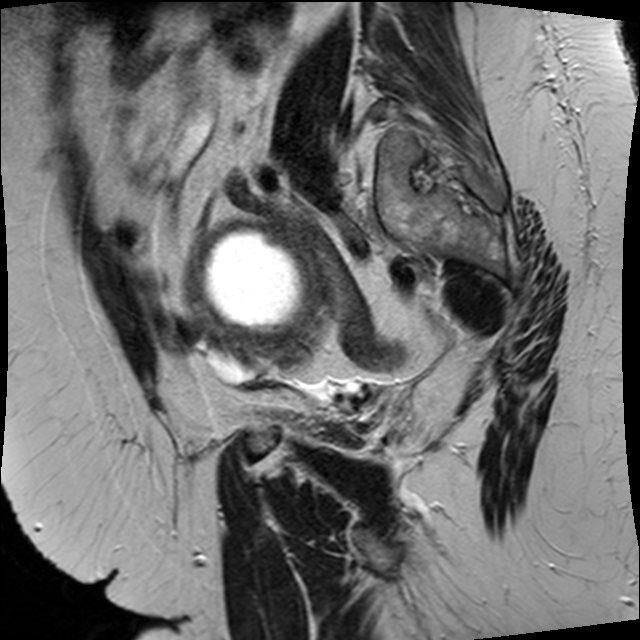
Pelvic MRI for cervical cancer, one sagittal slice. Position 26 of 34 along the scan axis. T2-weighted. 1.5 T. TE 89 ms, TR 3320 ms. 4 mm slice thickness. 640 × 640 image matrix. Female patient, age 50 years.
Outlined on this slice (outlined manually by an expert reader):
- uterus and cervix: bounding box (x1, y1, x2, y2) in pixels: (180, 219, 328, 353)